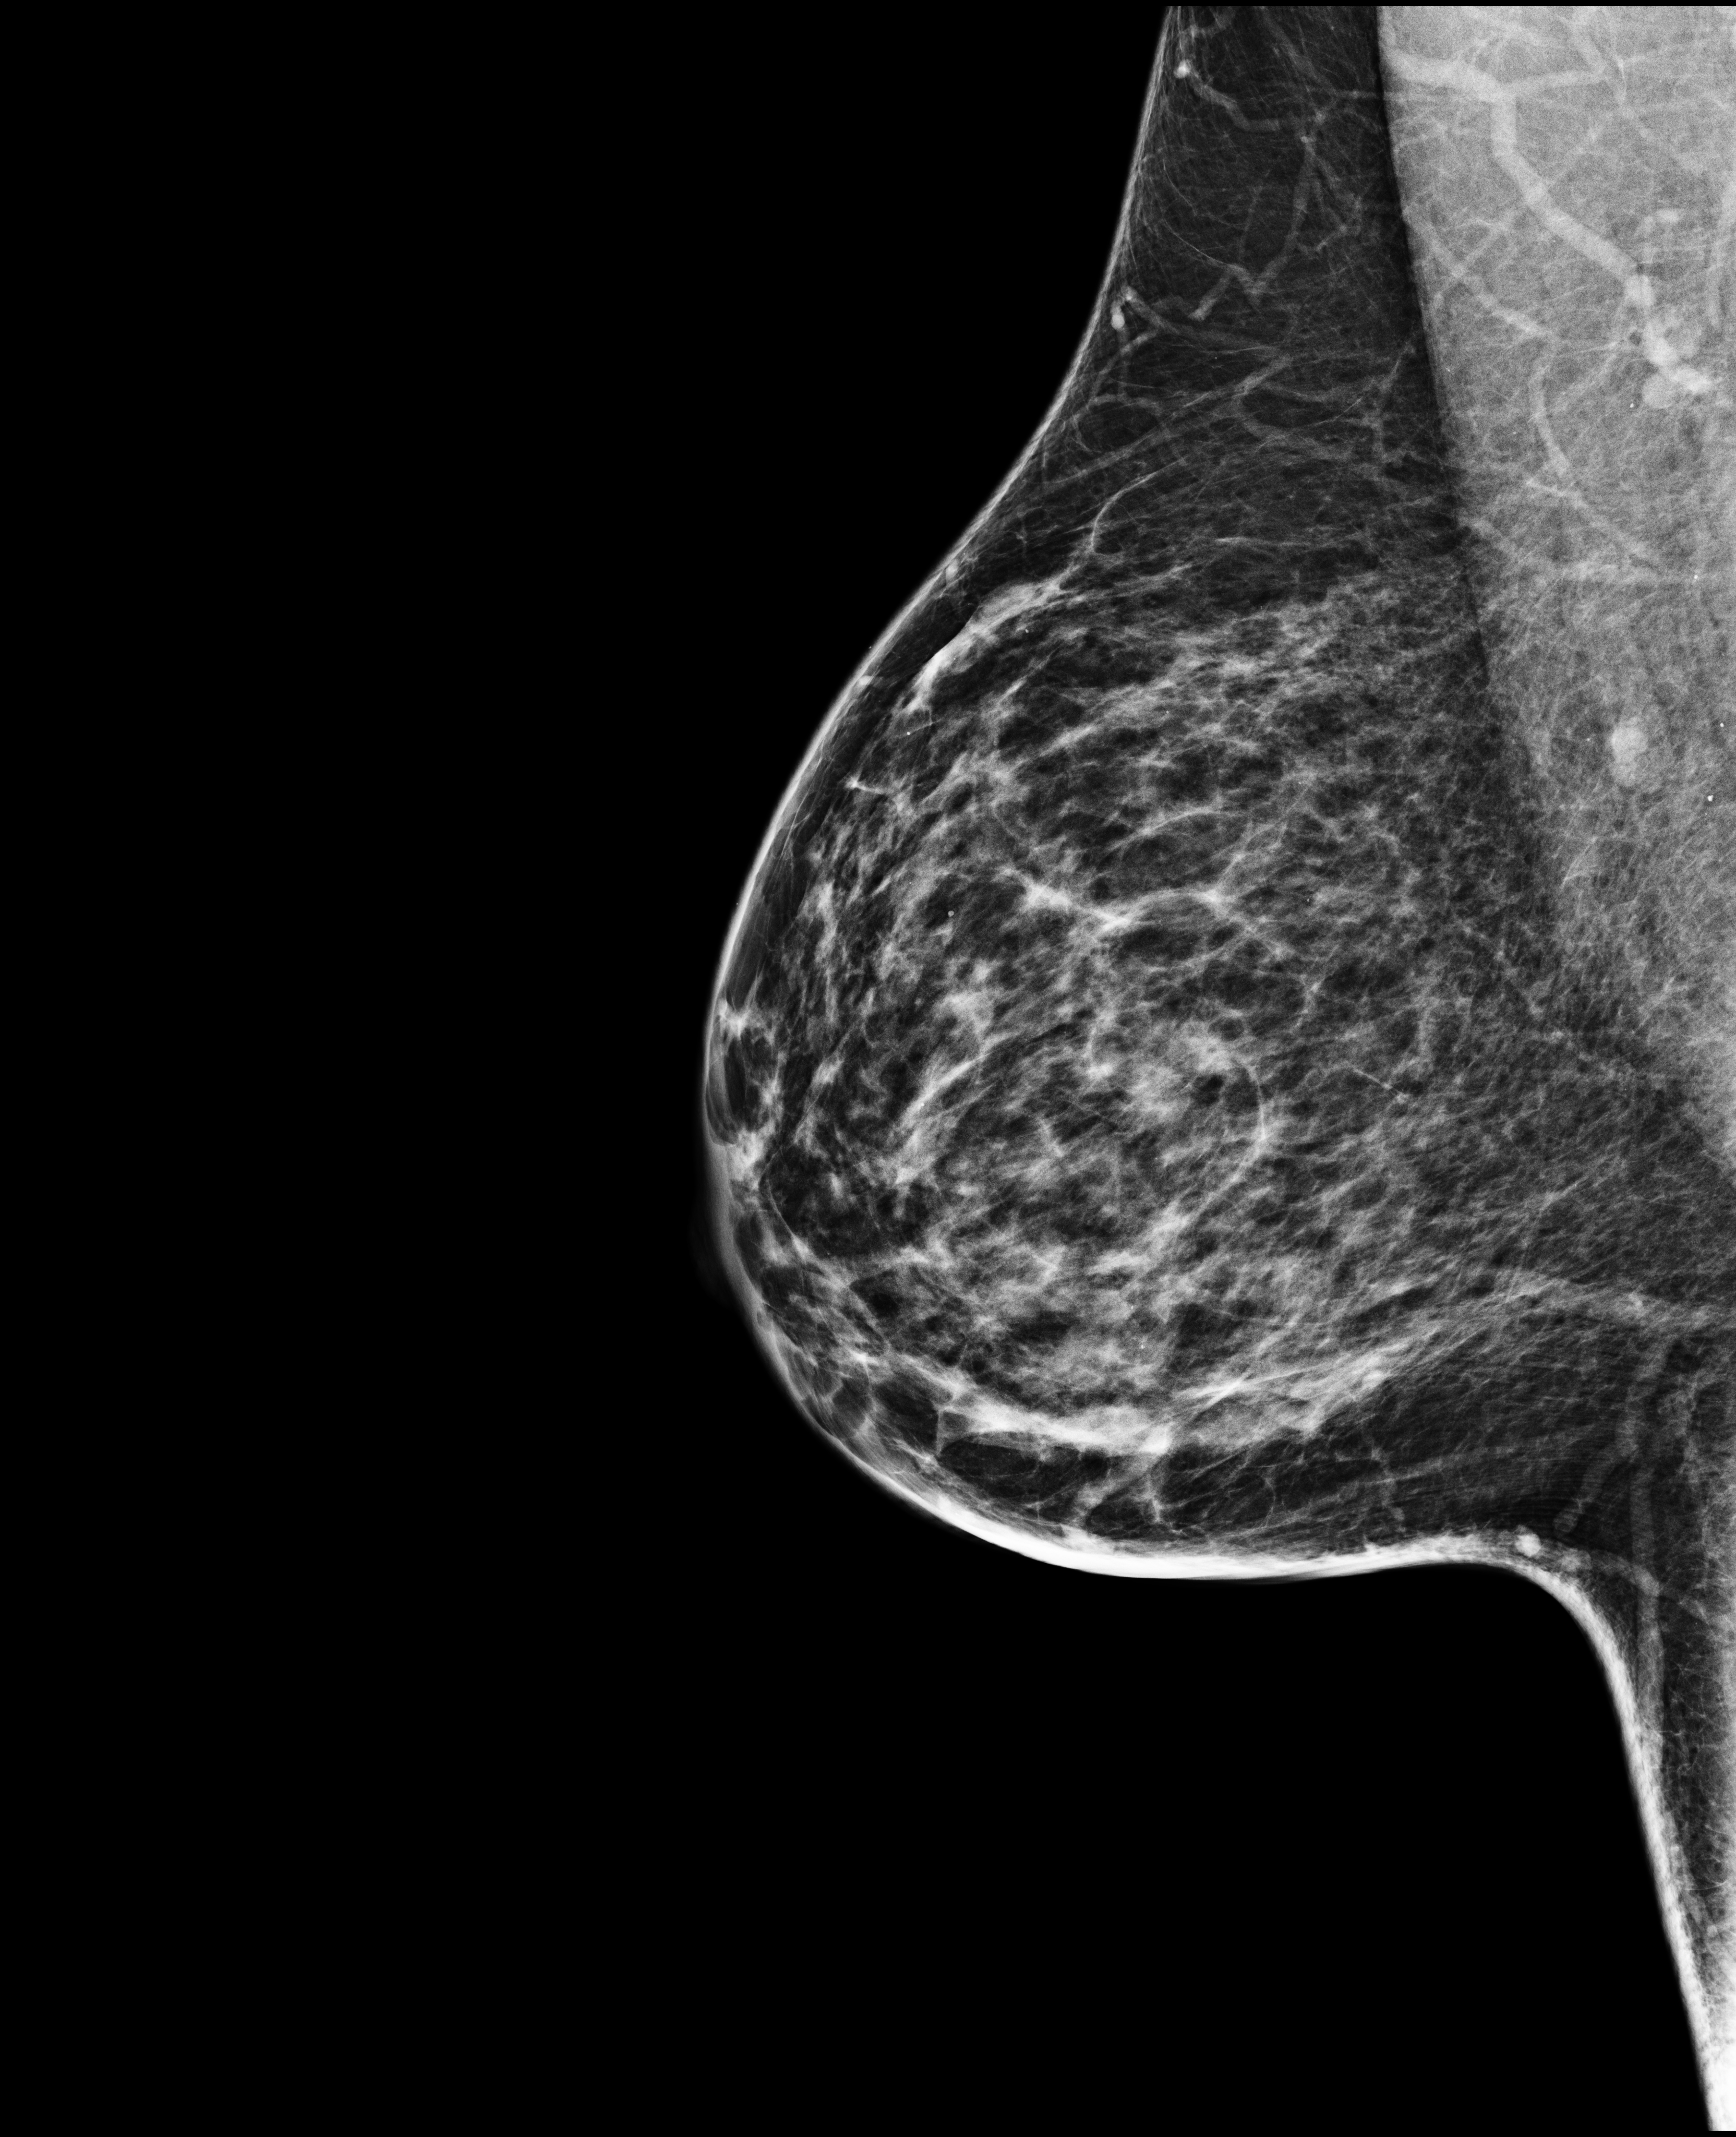
Annual screening mammography examination; compressed breast thickness 63 mm; system: Selenia Dimensions. Patient aged 49 years (female).
Image type: full-field digital mammogram. Breast: right. Projection: medio-lateral oblique projection.